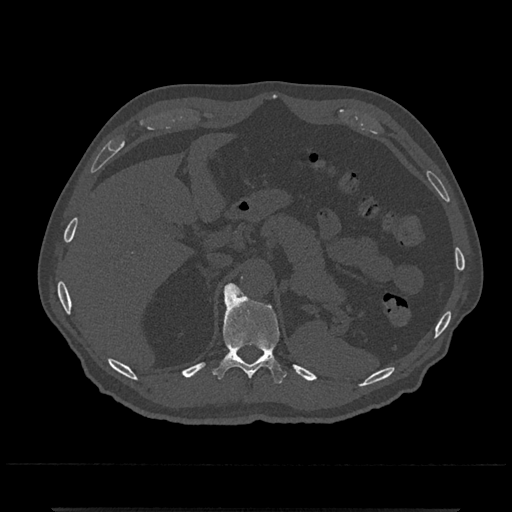
CT including the spine, one axial slice; slice 490 of 797 in the series (ordered by position); bone window (W 1800 / L 400 HU); 0.5 mm slice thickness; 512 × 512 image matrix. Patient: male, 67 years. From the clinical record (not read from this slice): primary cancer: prostate.
Outlined on this slice (semi-automatic segmentation, software-assisted and operator-edited):
- T11 vertebra: box from (x=213, y=284) to (x=287, y=384) px
- T12 vertebra: (x=228, y=284)–(x=241, y=291)